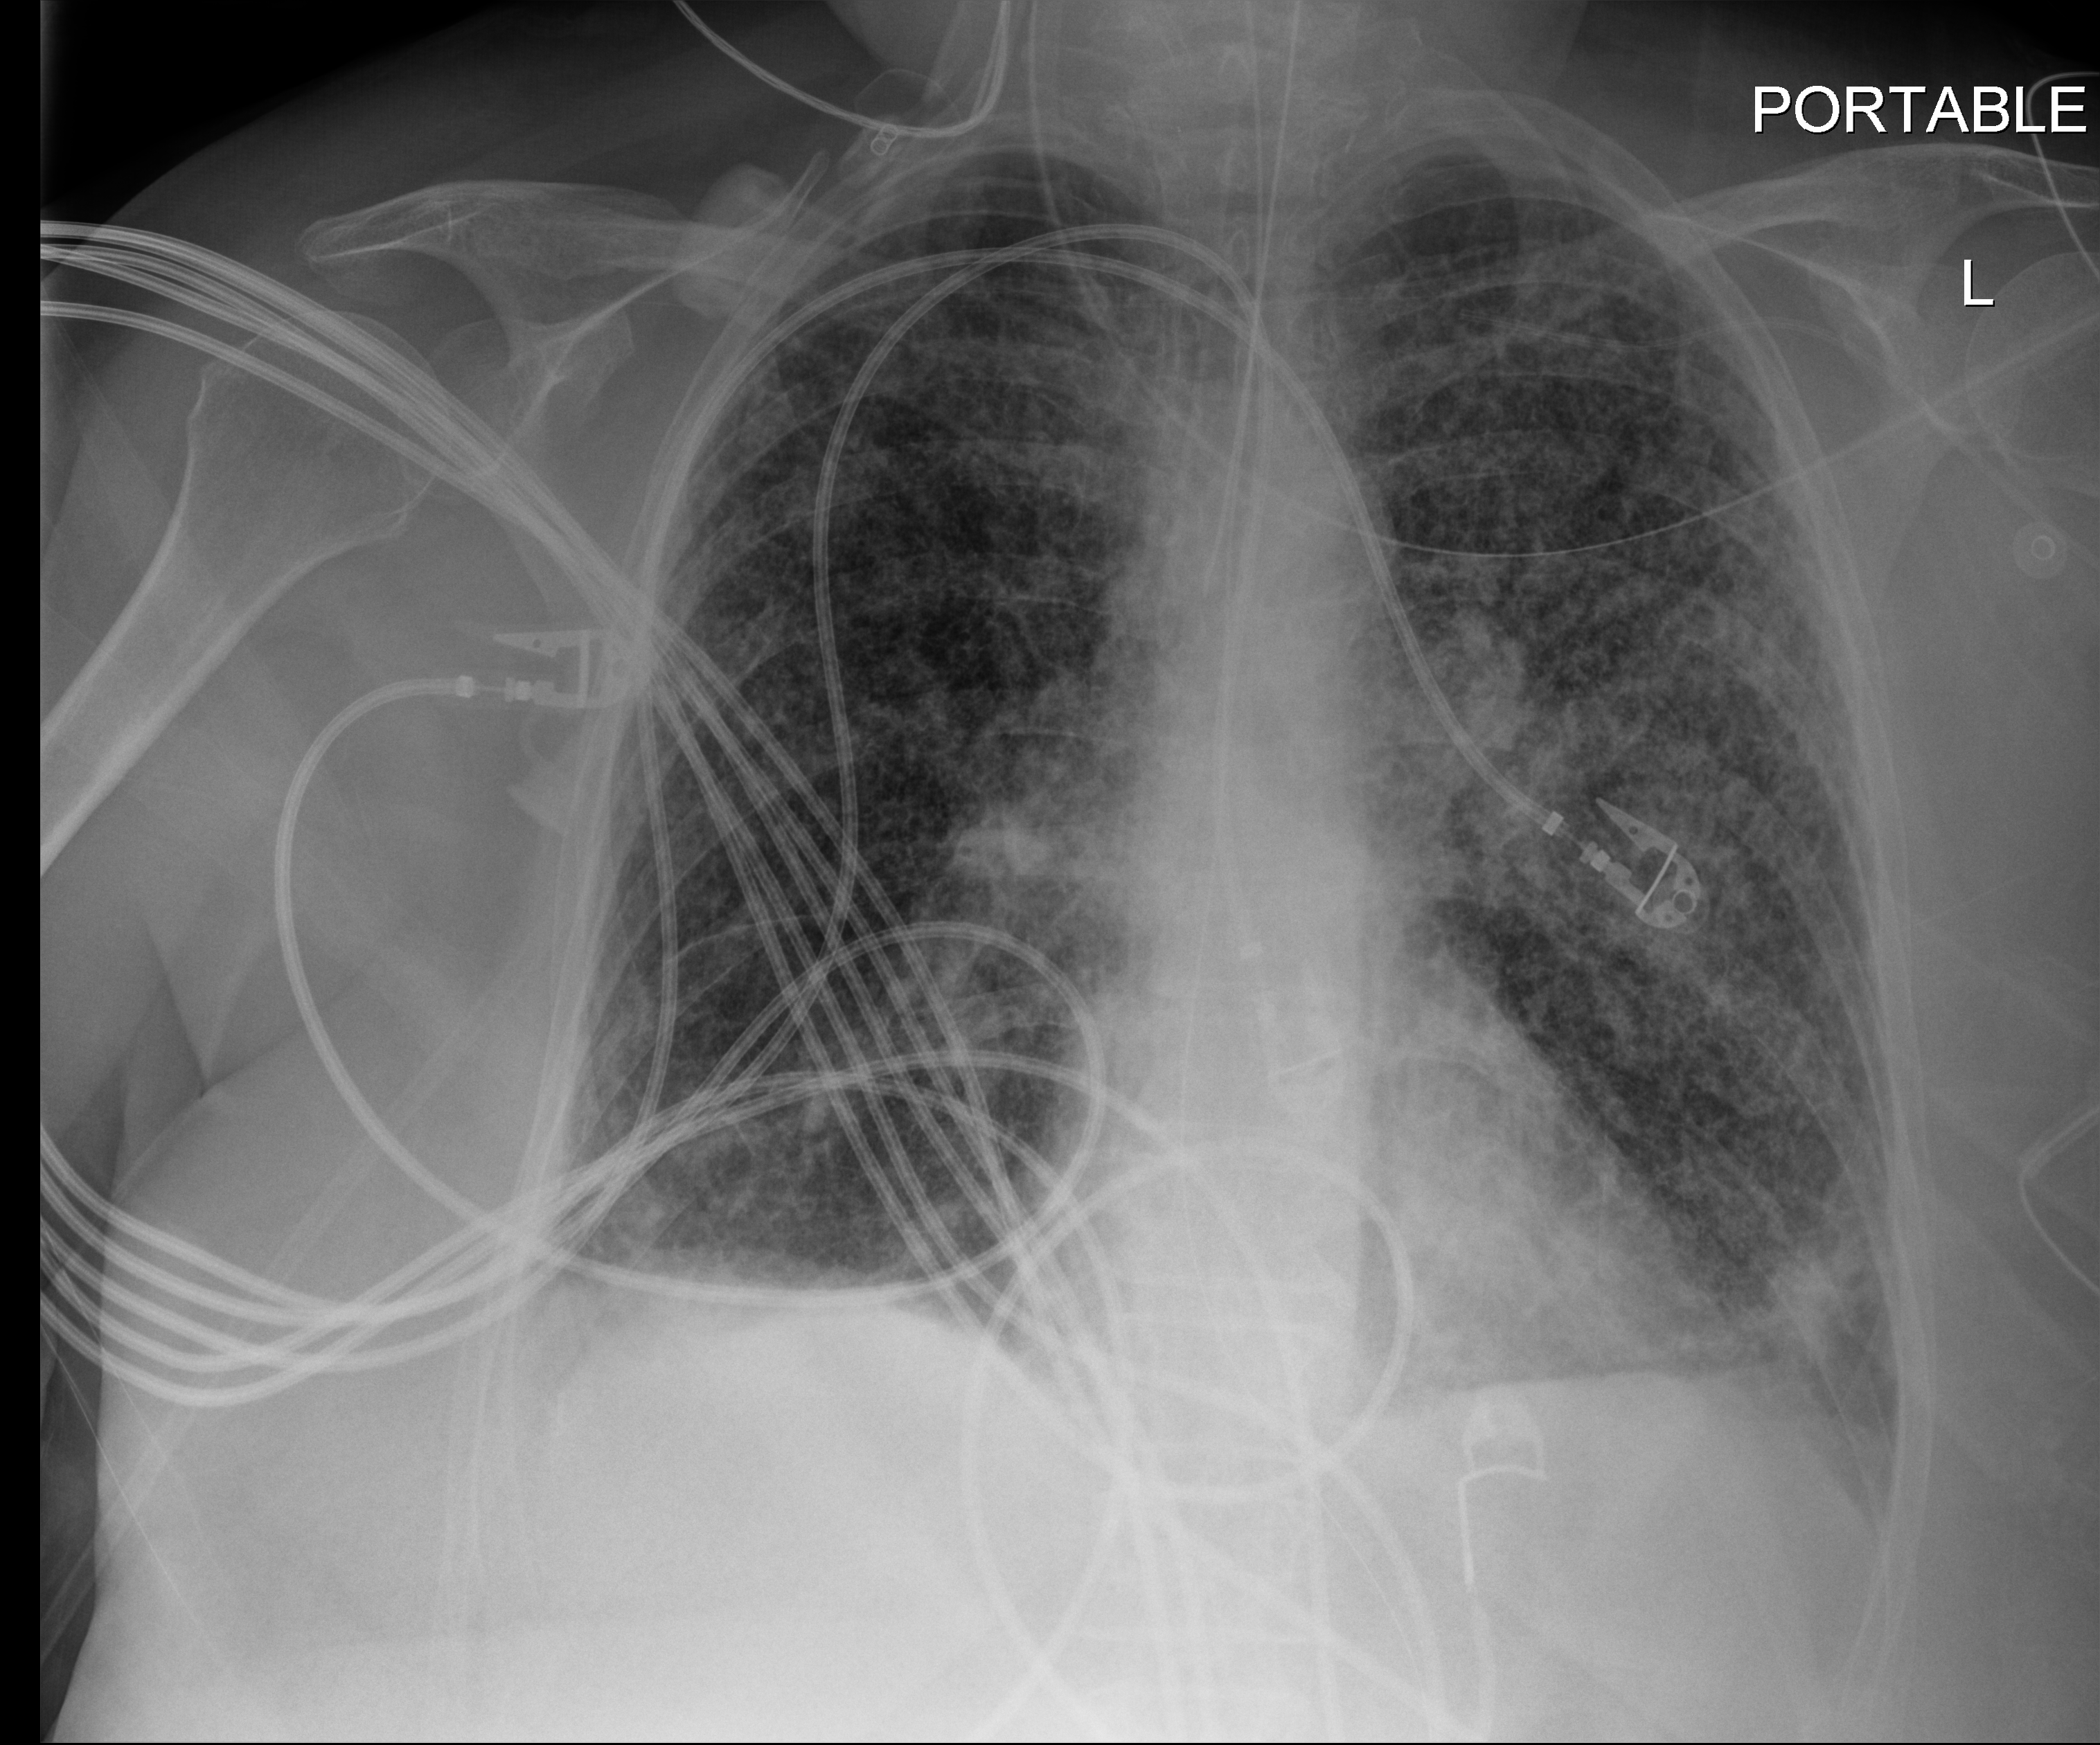
Chest radiograph (digital radiography). Patient hospitalised with COVID-19; female, aged 60–74 years.
Hospital-stay facts (about this admission, not read from this image; timing relative to this image not recorded):
- mechanically ventilated during this hospital stay: yes
- admitted to intensive care during this hospital stay: yes